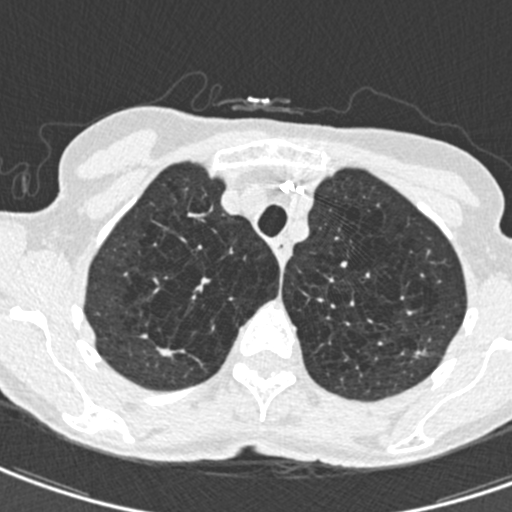
Low-dose screening chest CT, axial slice. Second screening round (one year after baseline). Lung window (W 1500 / L -600 HU). 0.75 mm slice thickness. Standard (soft-tissue) reconstruction kernel (B30f). Slice 104 of 498 in the series. Female, age 71 years at enrolment. Current smoker at enrolment.
Lesion marked by an expert reader, bounding box <405,332,444,370> (left, top, right, bottom; pixels). The screening reader recorded 2 non-calcified nodules or masses ≥4 mm on this exam (right upper lobe, left upper lobe); which of them this box marks is not recorded. Official screen result: positive, change unspecified: nodule(s) >= 4 mm or enlarging nodule(s), mass(es), or other non-specific abnormalities suspicious for lung cancer. Later outcome: lung cancer diagnosed 604 days after this screen — adenocarcinoma, NOS, left upper lobe, moderately differentiated (G2), stage IA (AJCC 6th edition), 12 mm at pathology.